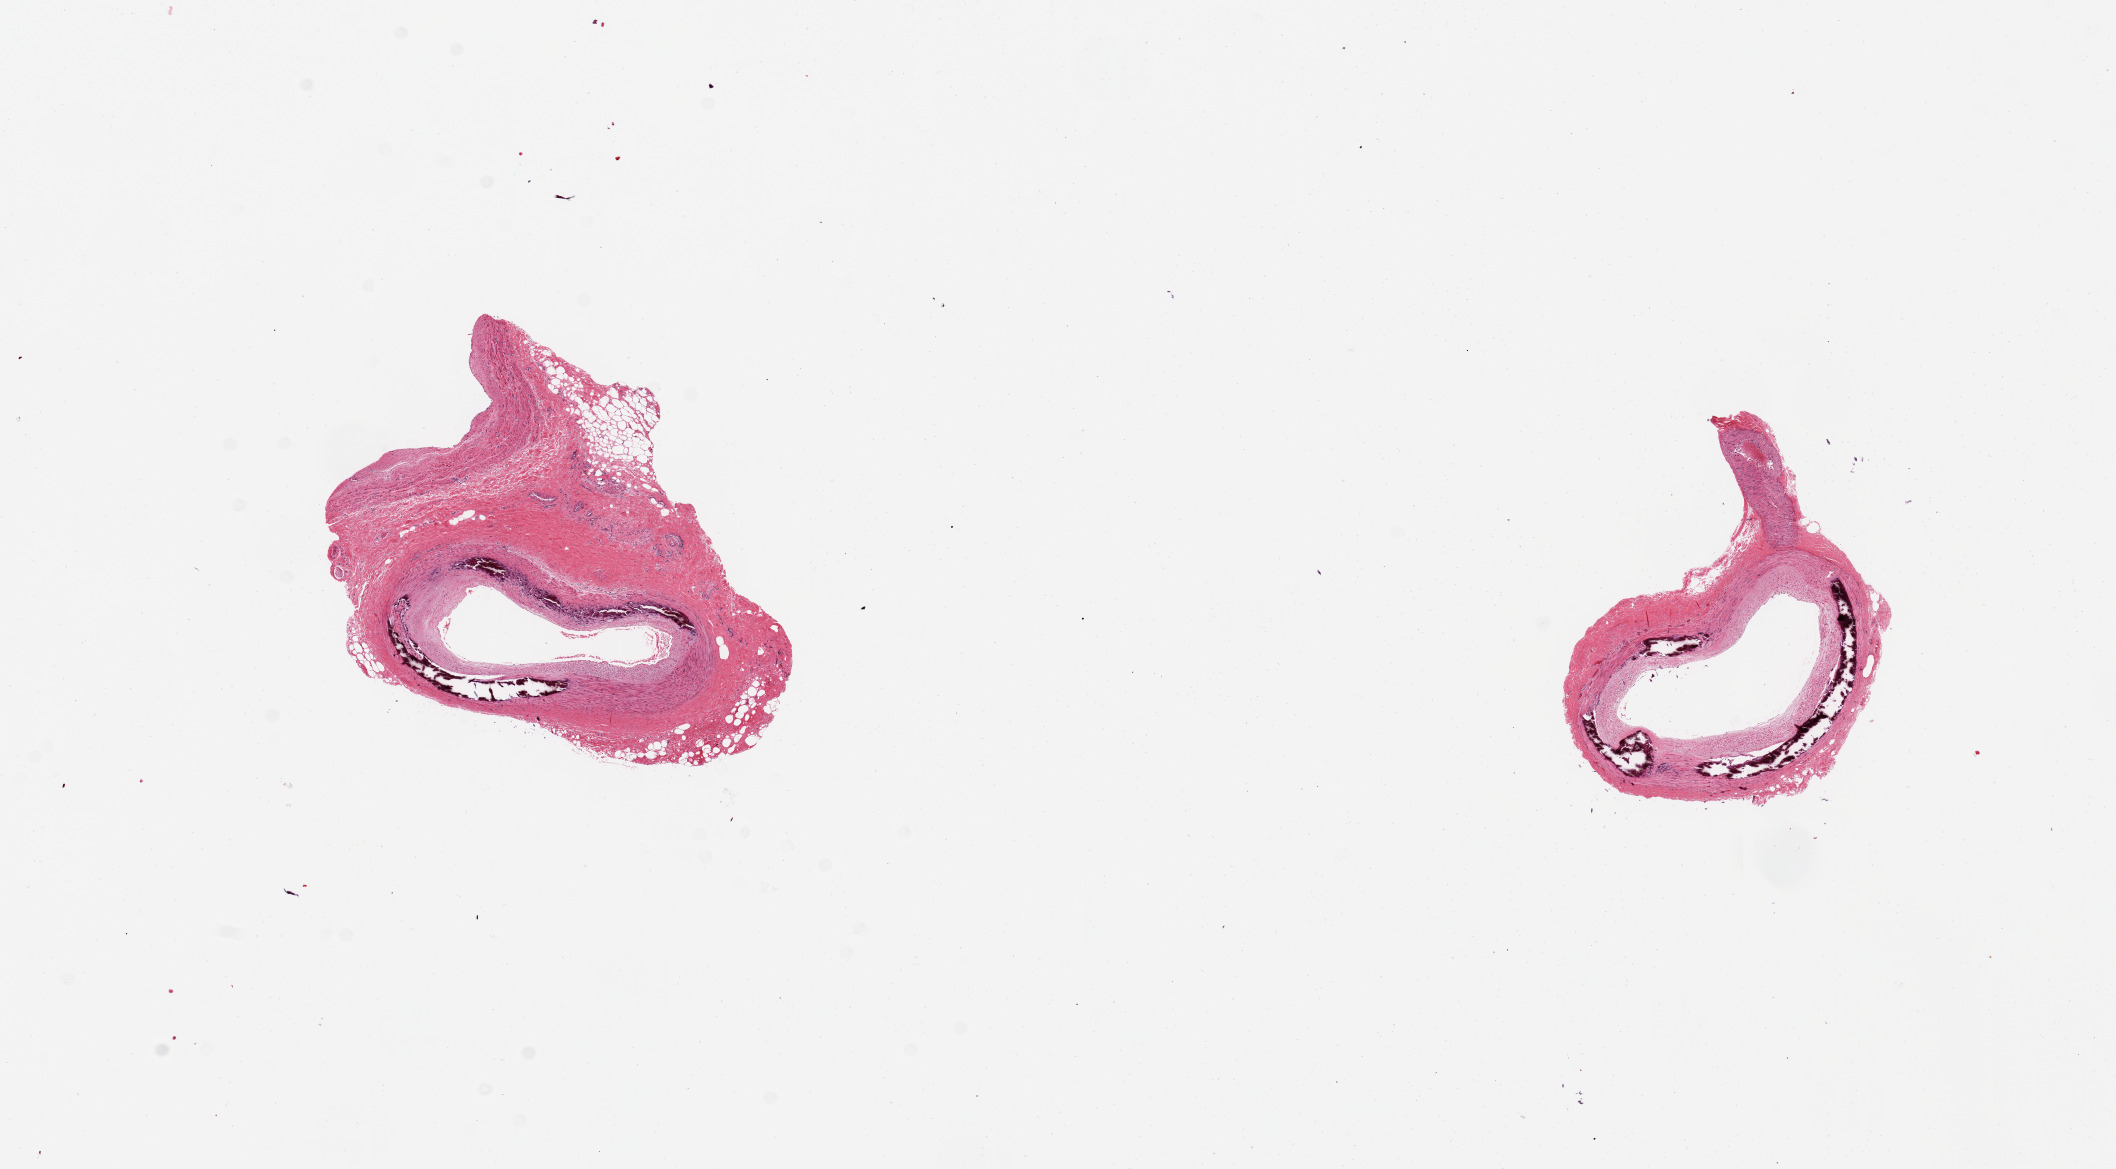
Whole-slide image, haematoxylin and eosin stain — whole scanned area (about 16.7 x 9.2 mm, slide scanned at 20x) shown as a low-resolution overview, PAXgene-fixed, paraffin-embedded tissue, section of tibial artery (target tissue), tissue donor sample. Donor: female.
Pathologist's review note for this sample: 2 pieces,adherent fibrofatty rim on one, ~1.5mm; both show Monckeberg medial sclerosis/calcifications/.